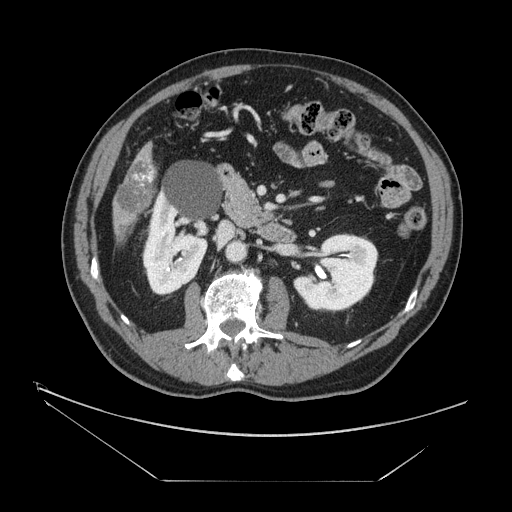
Contrast-enhanced abdominal CT, one axial slice; position 54 of 161 along the scan axis; 120 kVp; intravenous contrast given; soft-tissue window (W 400 / L 40 HU); 2.5 mm slice thickness; 512 × 512 image matrix, field of view 440 × 440 mm. Male patient, age 65 years. From the clinical record (not read from this slice): diagnosis: colorectal cancer liver metastases, imaged before liver resection; multiple liver metastases: yes; largest metastasis: 4.2 cm; disease in both lobes: yes.
Outlined on this slice (outlined manually by an expert reader):
- liver: box from (x=115, y=146) to (x=155, y=229) px
- portal vein (with intrahepatic branches): (x=136, y=173)–(x=152, y=180)
- liver metastasis: (x=123, y=226)–(x=127, y=235)
- liver metastasis: (x=117, y=163)–(x=154, y=214)